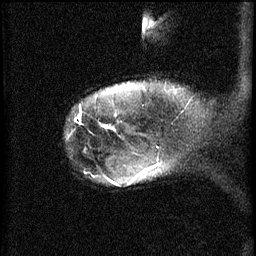
Breast MRI (dynamic contrast-enhanced), one sagittal slice. Position 55 of 60 along the scan axis. 3 images stored at this slice position (order not interpretable as contrast timing). 1.5 T. TE 4.2 ms, TR 11 ms. 256 × 256 image matrix, field of view 180 × 180 mm. Female patient, age 44 years.
Structures marked on this image (semi-automatic segmentation, software-assisted and operator-edited):
- analysis volume of interest (the breast-tissue region the enhancement analysis was run in; not a lesion): bounding box [x1, y1, x2, y2] px = [110, 128, 165, 179]
- tumour enhancement mask (voxels above the 70 % enhancement threshold inside the analysis volume of interest): [134, 164, 157, 179]